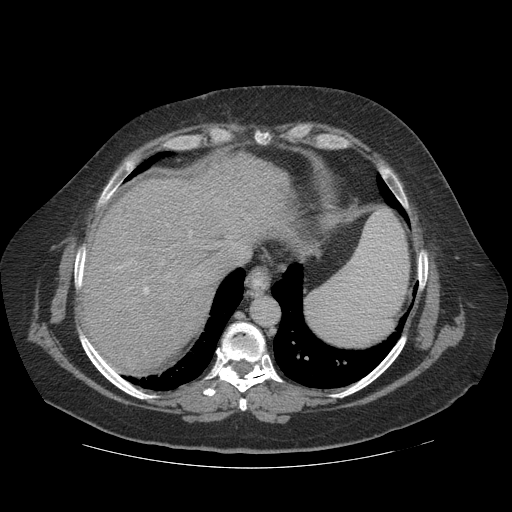
Contrast-enhanced abdominal CT (liver protocol), one axial slice; slice 97 of 121 in the series (ordered by position); reconstruction kernel STANDARD; 140 kVp; soft-tissue window (W 400 / L 40 HU); 2.5 mm slice thickness; 512 × 512 image matrix, field of view 420 × 420 mm. From the clinical record (not read from this slice): diagnosis: hepatocellular carcinoma (patient treated with transarterial chemoembolisation; whether this scan precedes or follows treatment is not stated here); TNM stage (as recorded): Stage-IIIA; Child-Pugh class: A; tumour nodularity: multinodular; tumour size: 7.4 cm.
Annotated regions visible in this slice (semi-automatically segmented with operator editing):
- abdominal aorta: bounding box (x1, y1, x2, y2) in pixels: (252, 298, 279, 327)
- liver parenchyma outside the tumour (the mass and vessels are separate outlines, so this box may not span the whole liver): (81, 154, 292, 372)
- liver vessels: (118, 201, 197, 295)